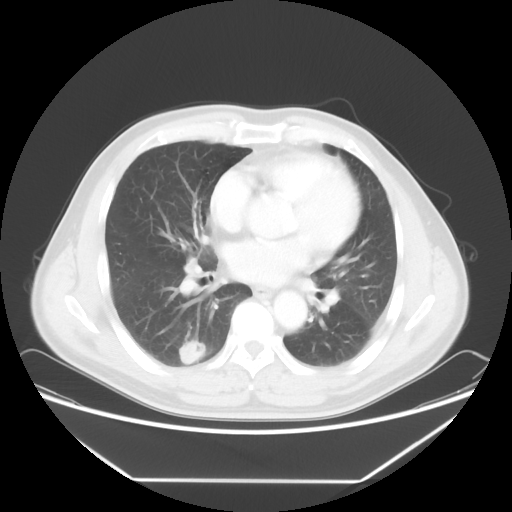
Chest CT, one axial slice; slice 33 of 65 in the series (ordered by position); reconstruction kernel STANDARD; 120 kVp; lung window (W 1500 / L -600 HU); 5 mm slice thickness; 512 × 512 image matrix, field of view 418 × 418 mm. Male patient, age 50 years. Case-level facts recorded for this patient, not image findings: clinical TNM (as recorded): T1c N0 M0; histopathological grade: G3.
Outlined on this slice (rectangle marked by the reading radiologist):
- lung tumour (recorded histology: adenocarcinoma): box from (x=177, y=336) to (x=215, y=370) px